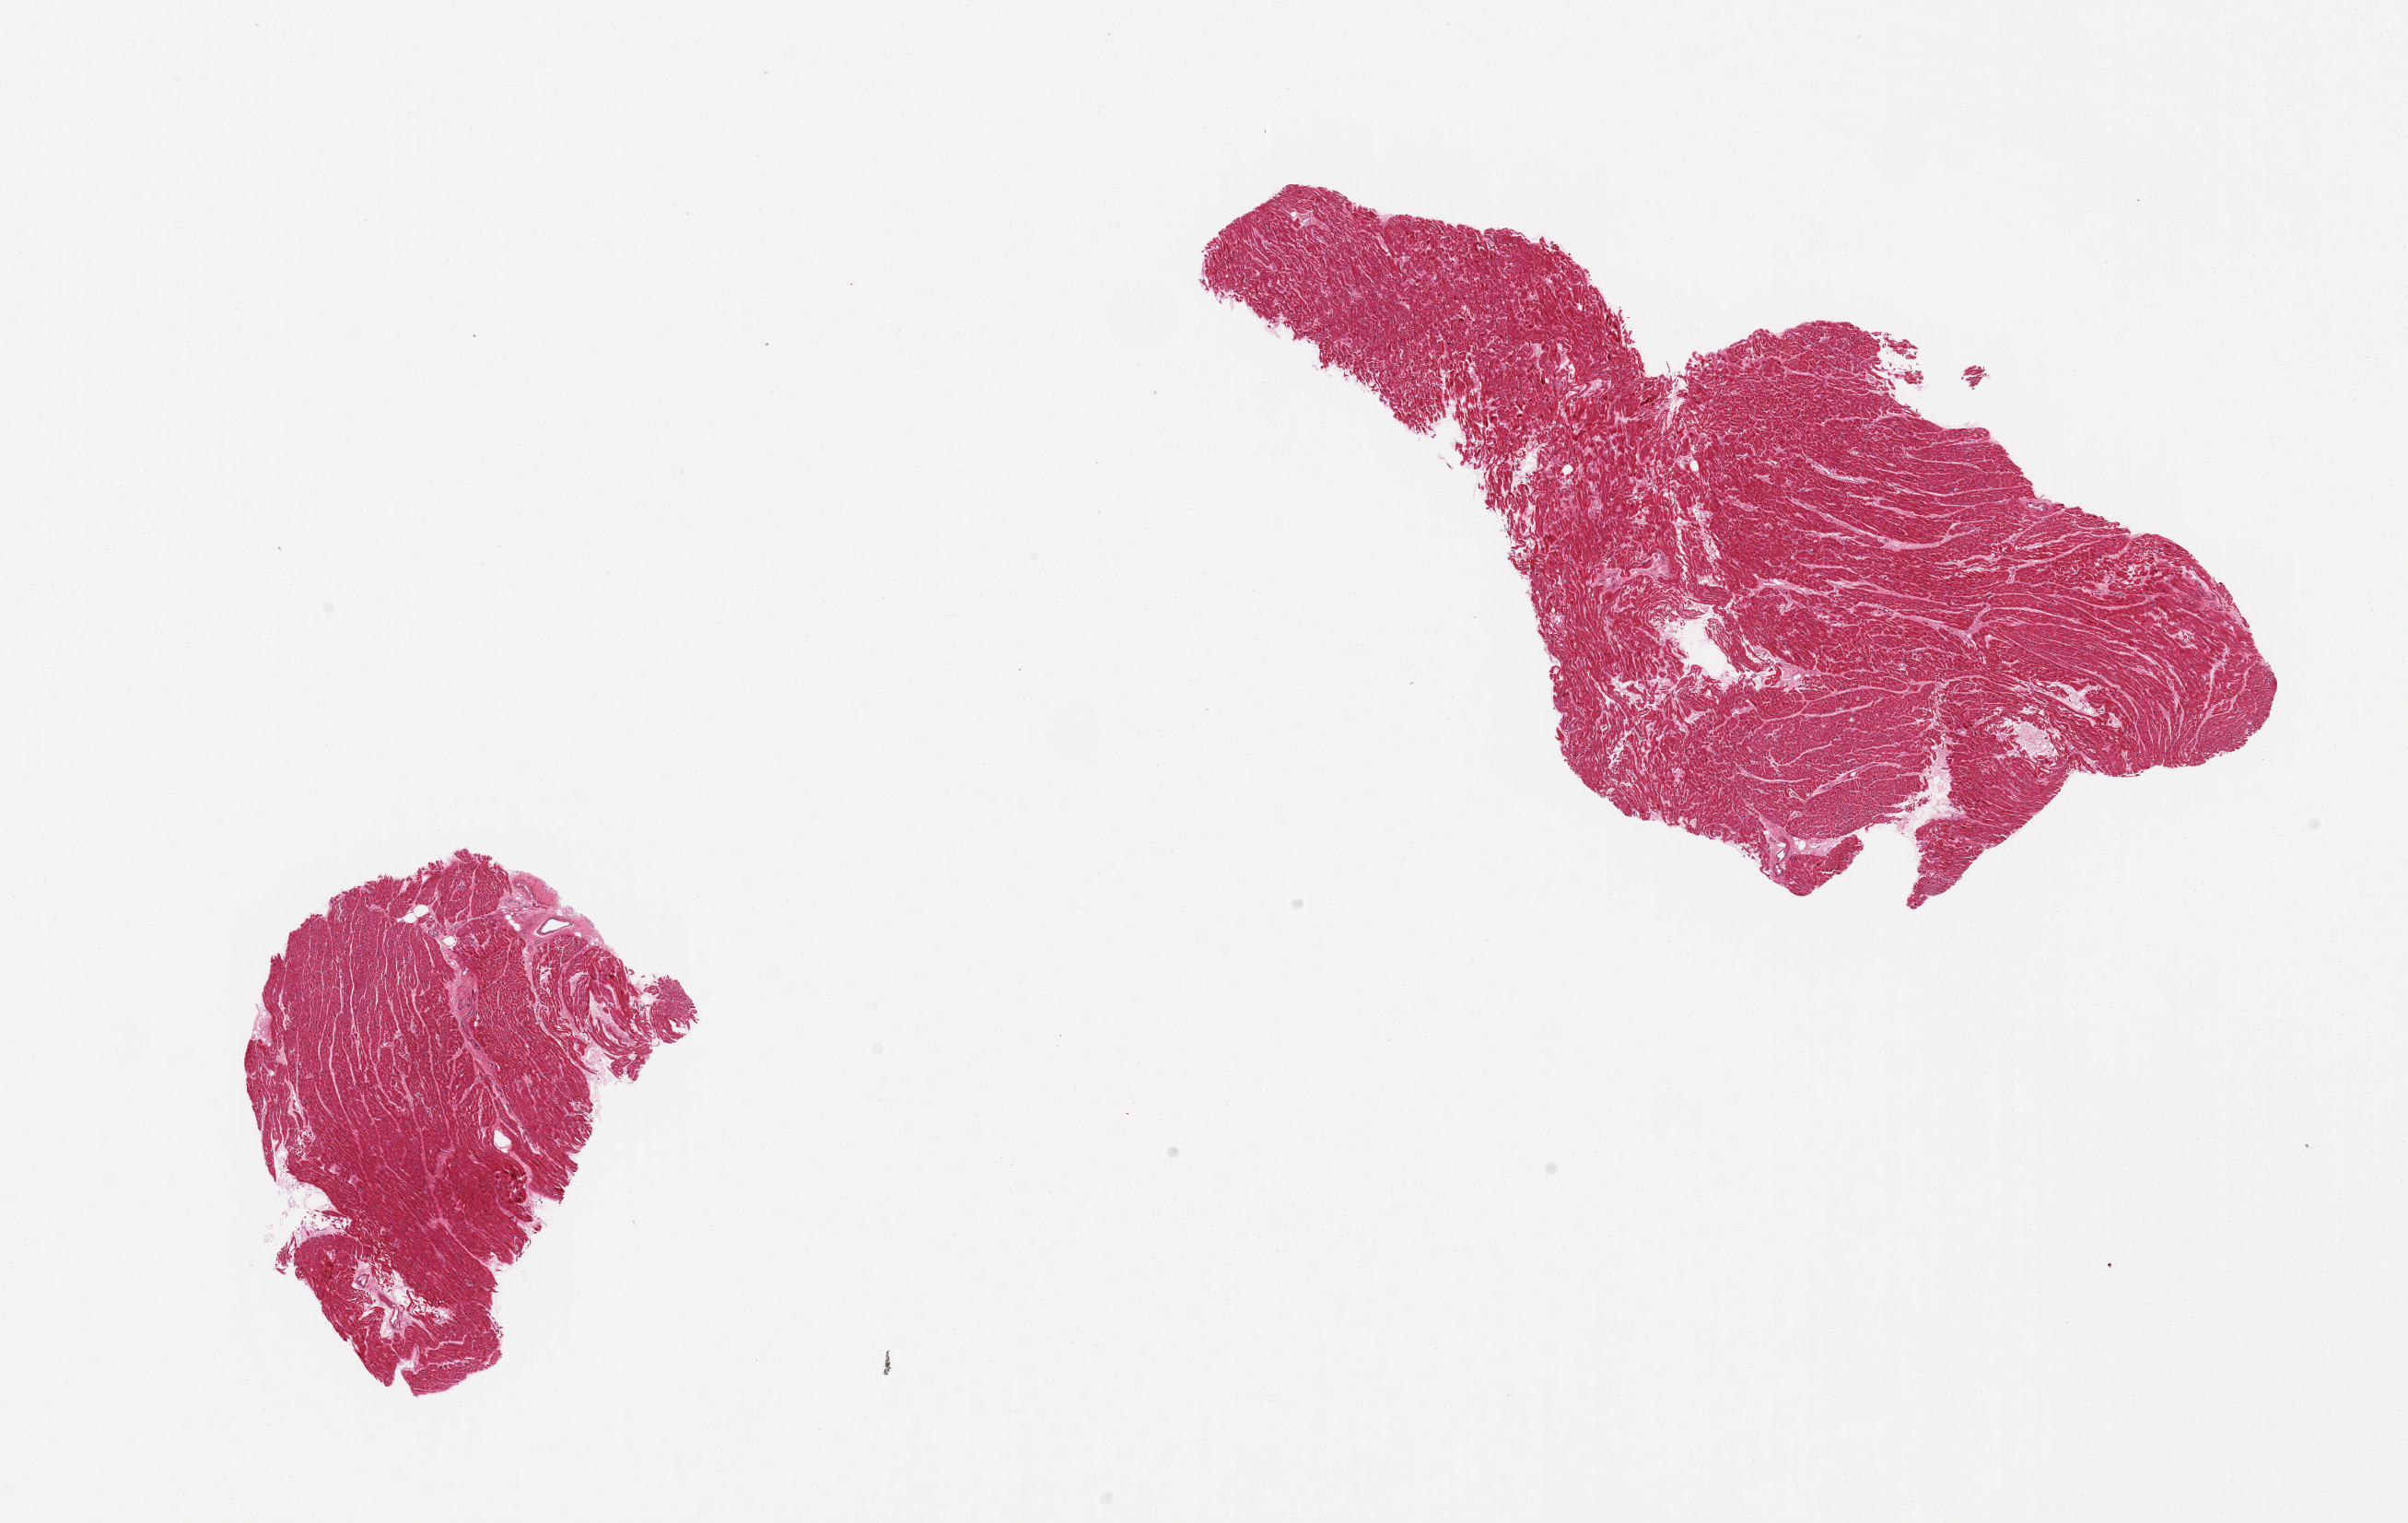
Whole-slide image, hematoxylin and eosin (H&E) stain, brightfield, shown as a low-resolution overview of the whole scanned area (about 20.7 x 13.1 mm, slide scanned at 20x); PAXgene-fixed, paraffin-embedded tissue; target tissue: heart; tissue donor sample. Male donor.
- review note (as recorded): 2 small irregular pieces (3x4 & 9x4mm)